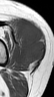
MRI of an extremity soft-tissue mass, one axial slice. Position 27 of 42 along the scan axis. MR volume resampled by the dataset authors to the PET/CT grid (not the native acquisition matrix). 3.27 mm slice thickness. 54 × 97 image matrix. Female patient. Case-level facts recorded for this patient, not image findings: histological type: spindle cell suggestive of biphasic synovial sarcoma; grade: intermediate; site of the primary tumour: left knee.
Structures marked on this image (expert contour drawn on MRI and transferred to this co-registered scan by the dataset authors):
- gross tumour volume including surrounding oedema: box from (x=19, y=19) to (x=45, y=65) px
- gross tumour volume (mass): (x=19, y=19)–(x=45, y=65)